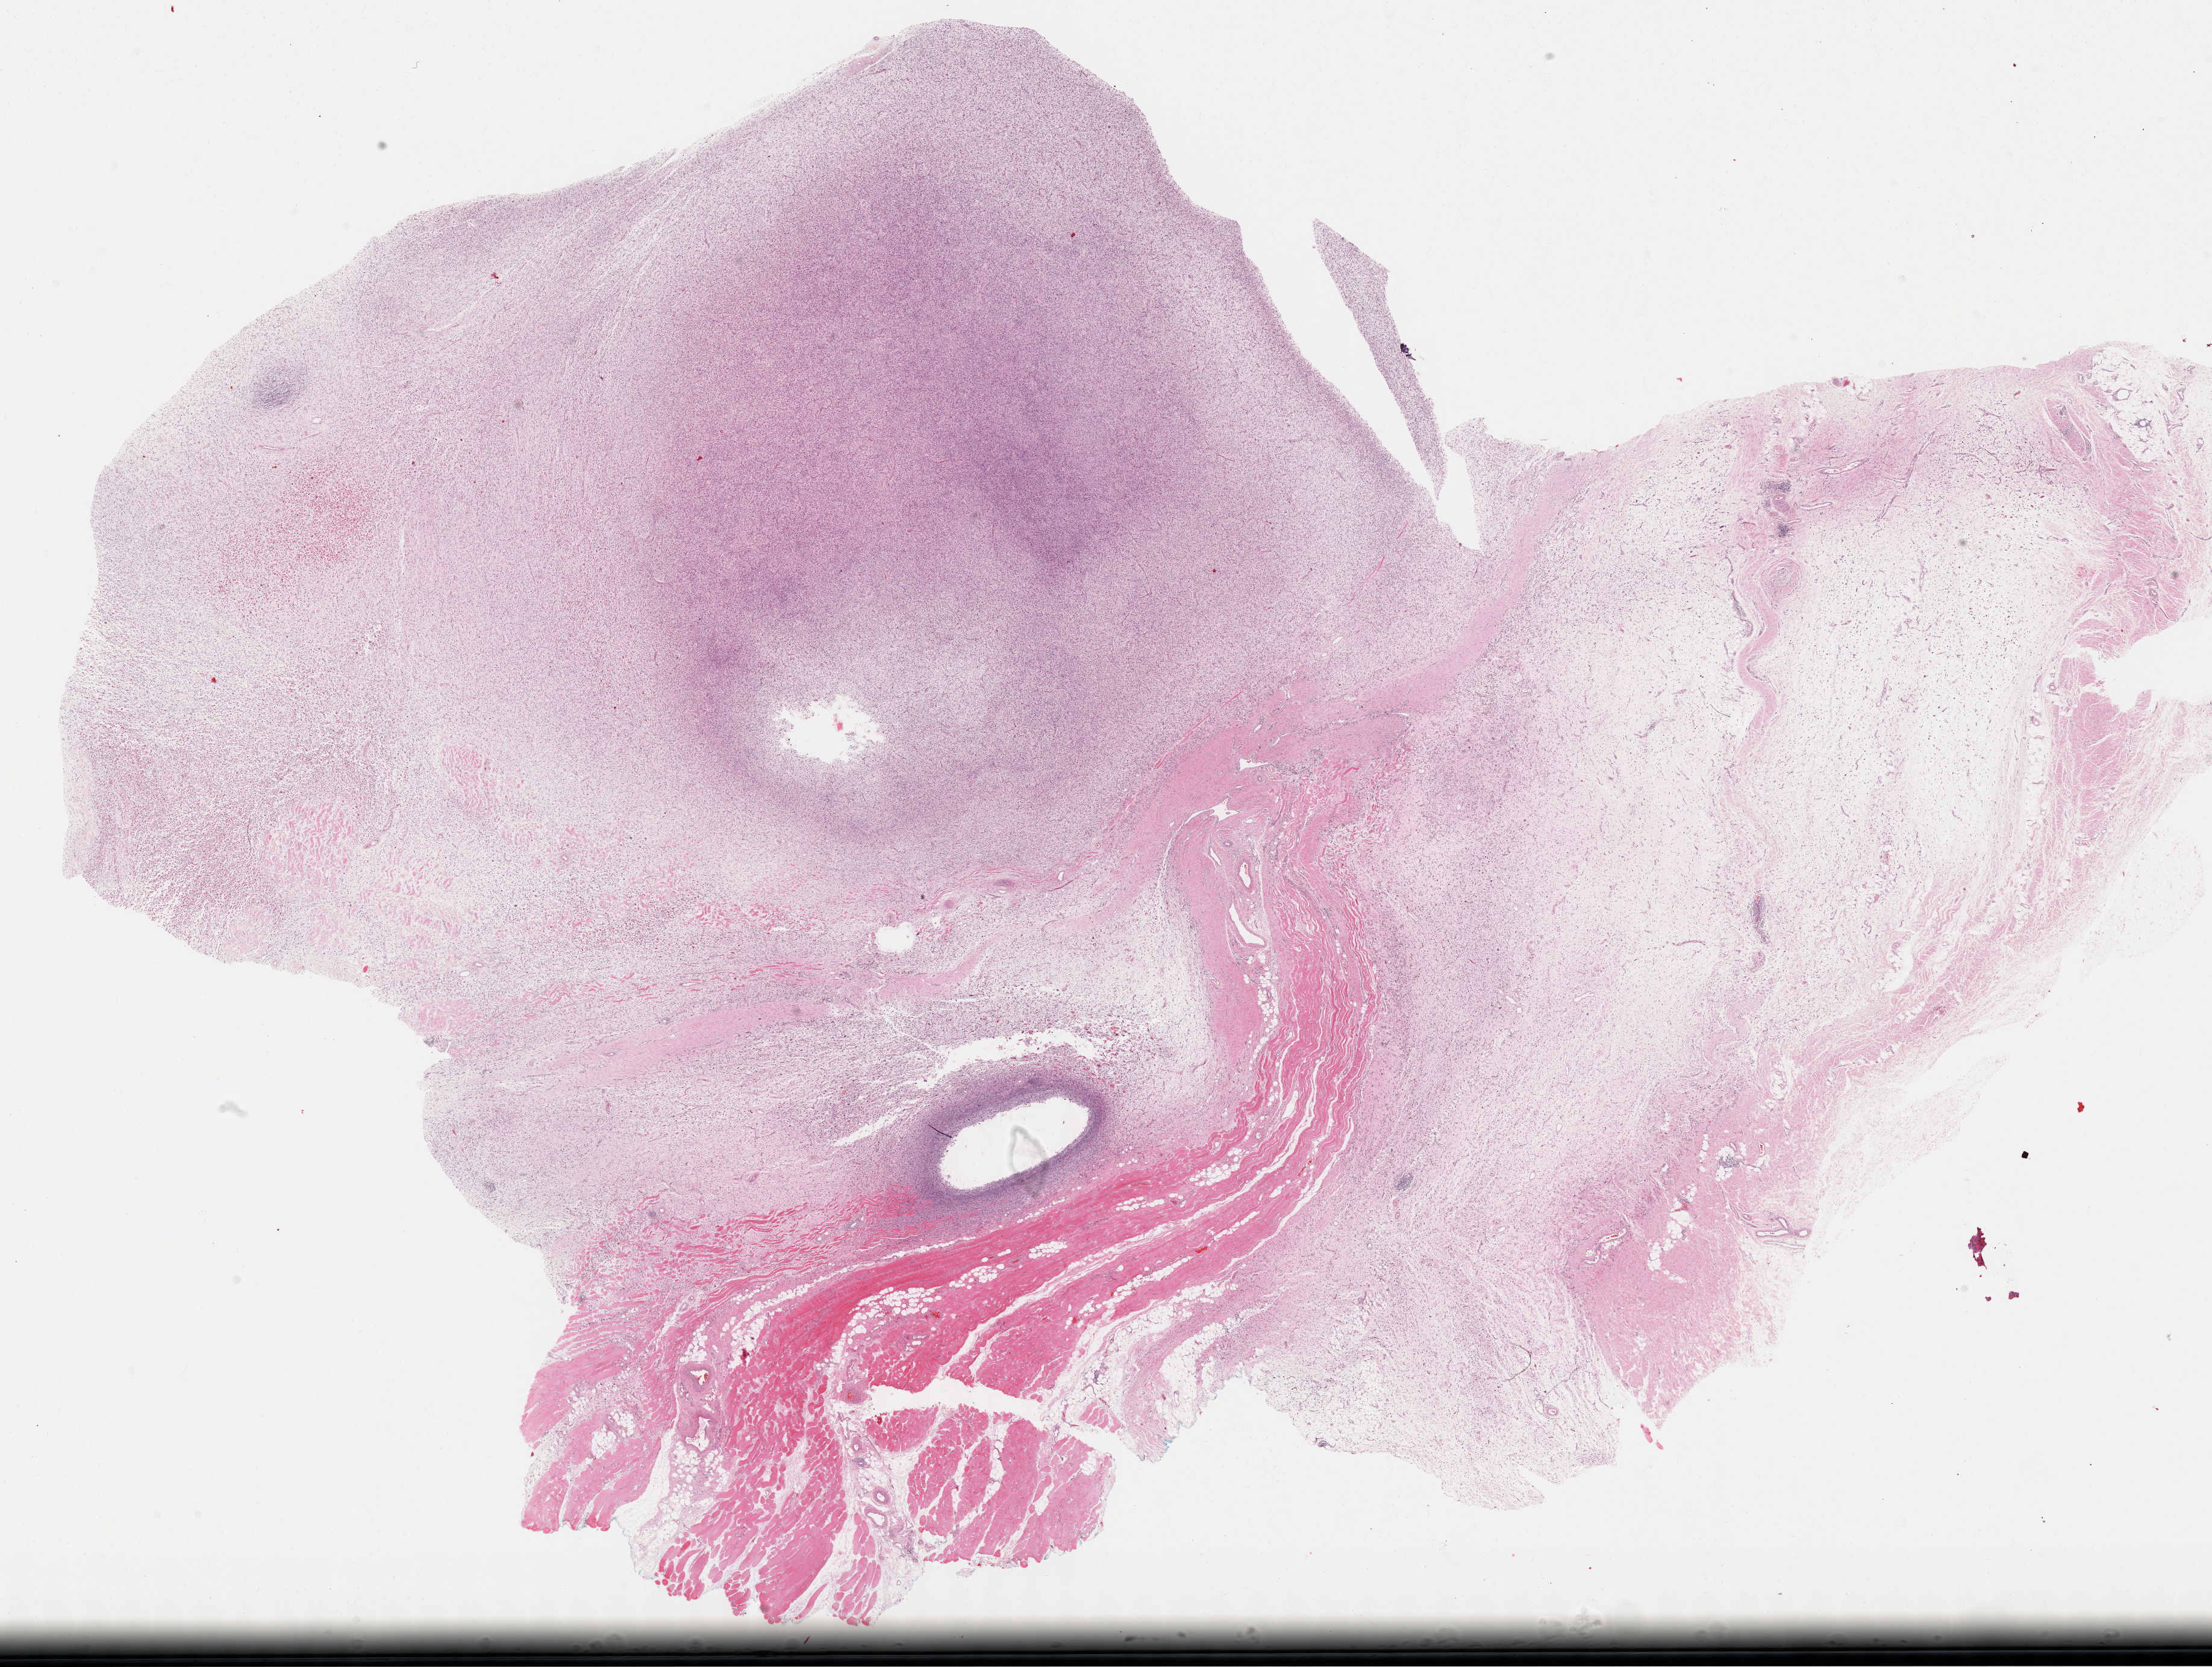
H&E-stained whole-slide image — a low-resolution overview of the entire scanned area, about 29.7 x 22.4 mm (slide scanned at 40x); formalin-fixed paraffin-embedded (FFPE) diagnostic section; sample: primary tumour, connective, subcutaneous and other soft tissues. Patient: female, age at initial diagnosis 54 years.
- pathologic diagnosis: Fibromyxosarcoma (connective, subcutaneous and other soft tissues of lower limb and hip)